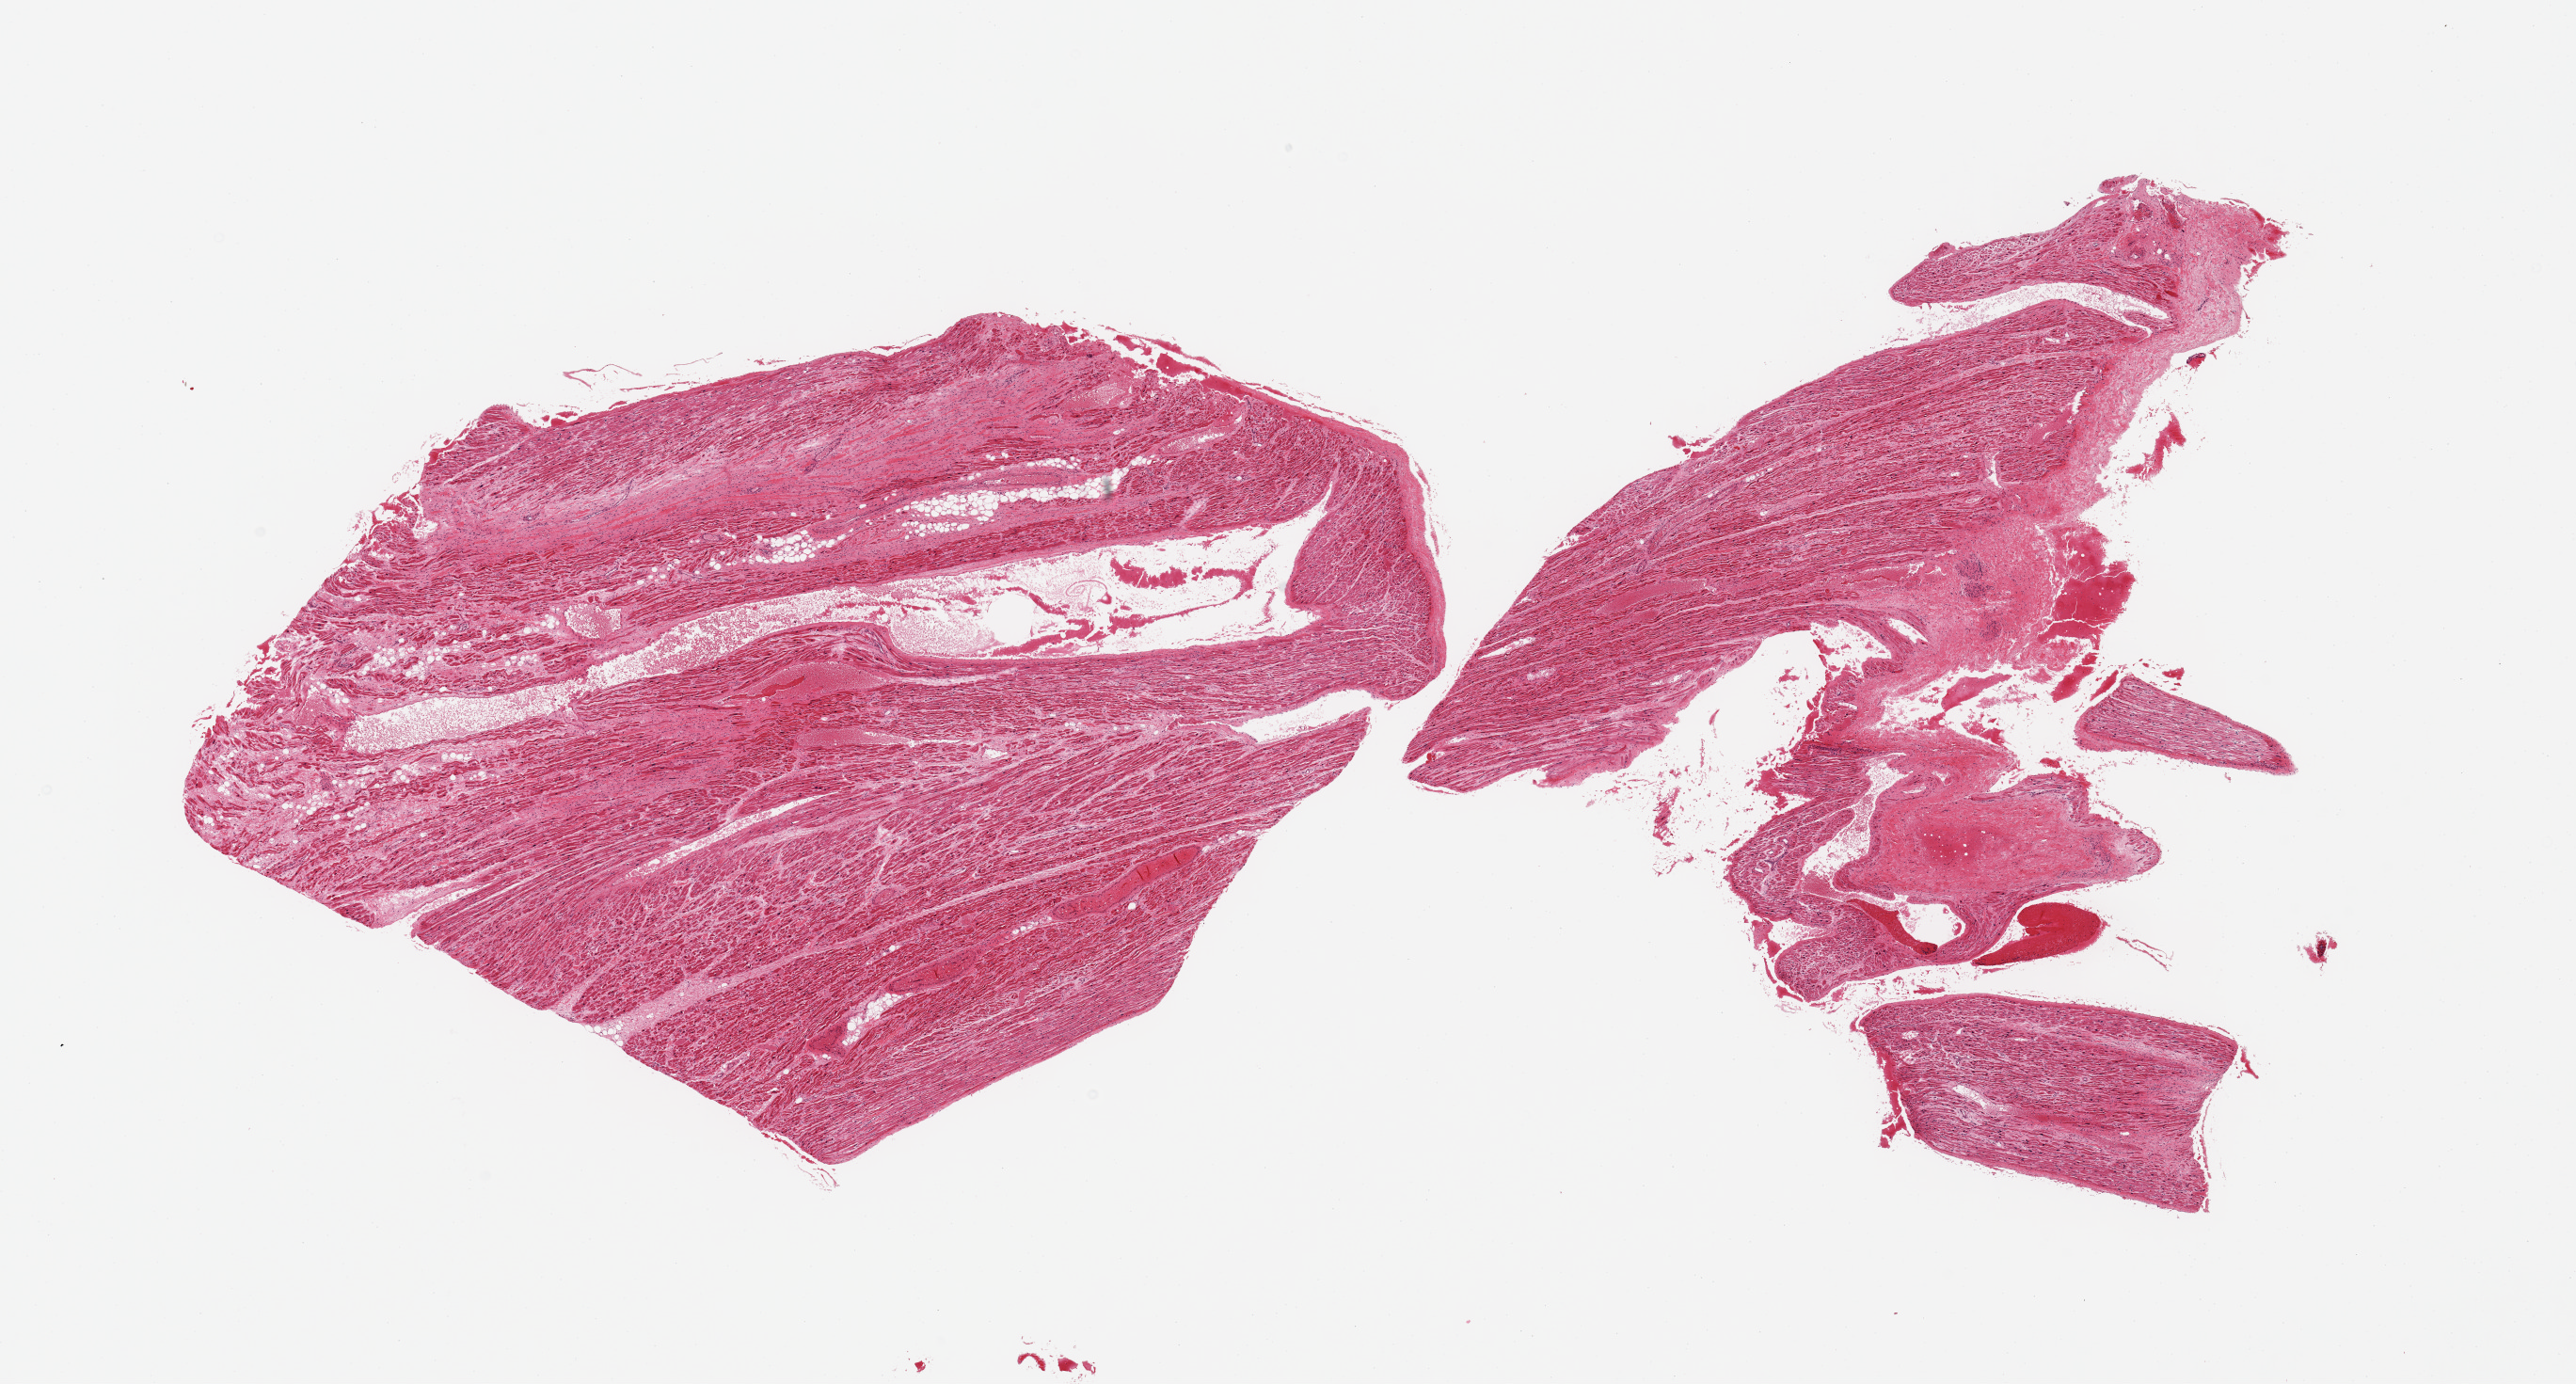
Hematoxylin and eosin (H&E) whole-slide image — low-resolution overview of the scanned area, about 21.7 x 11.6 mm, PAXgene-fixed, paraffin-embedded tissue, section of auricular appendage (target tissue), tissue donor sample. Donor: male.
Reviewer comment on this tissue sample: 2 pieces, no abnormalities.